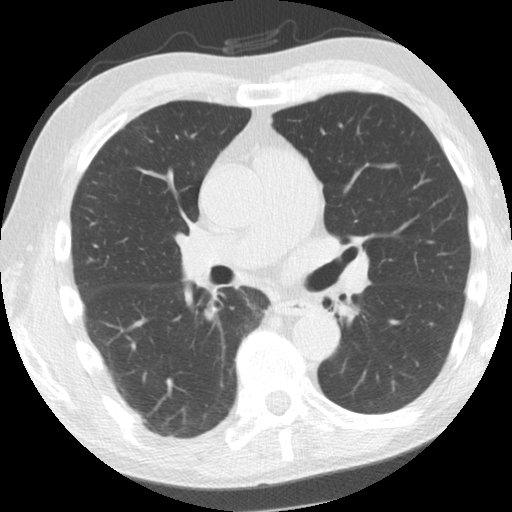
Chest CT (low-dose screening protocol), one axial image, second annual screen, lung window (W 1500 / L -600 HU), 2.5 mm slice thickness, 120 kVp. Male participant, aged 61 years at enrolment. Former smoker at enrolment.
Expert-annotated lung lesion, box from (x=301, y=289) to (x=347, y=326) px. No non-calcified nodule or mass ≥4 mm was recorded by the screening reader at this exam. Official screen result: negative screen, minor abnormalities not suspicious for lung cancer.